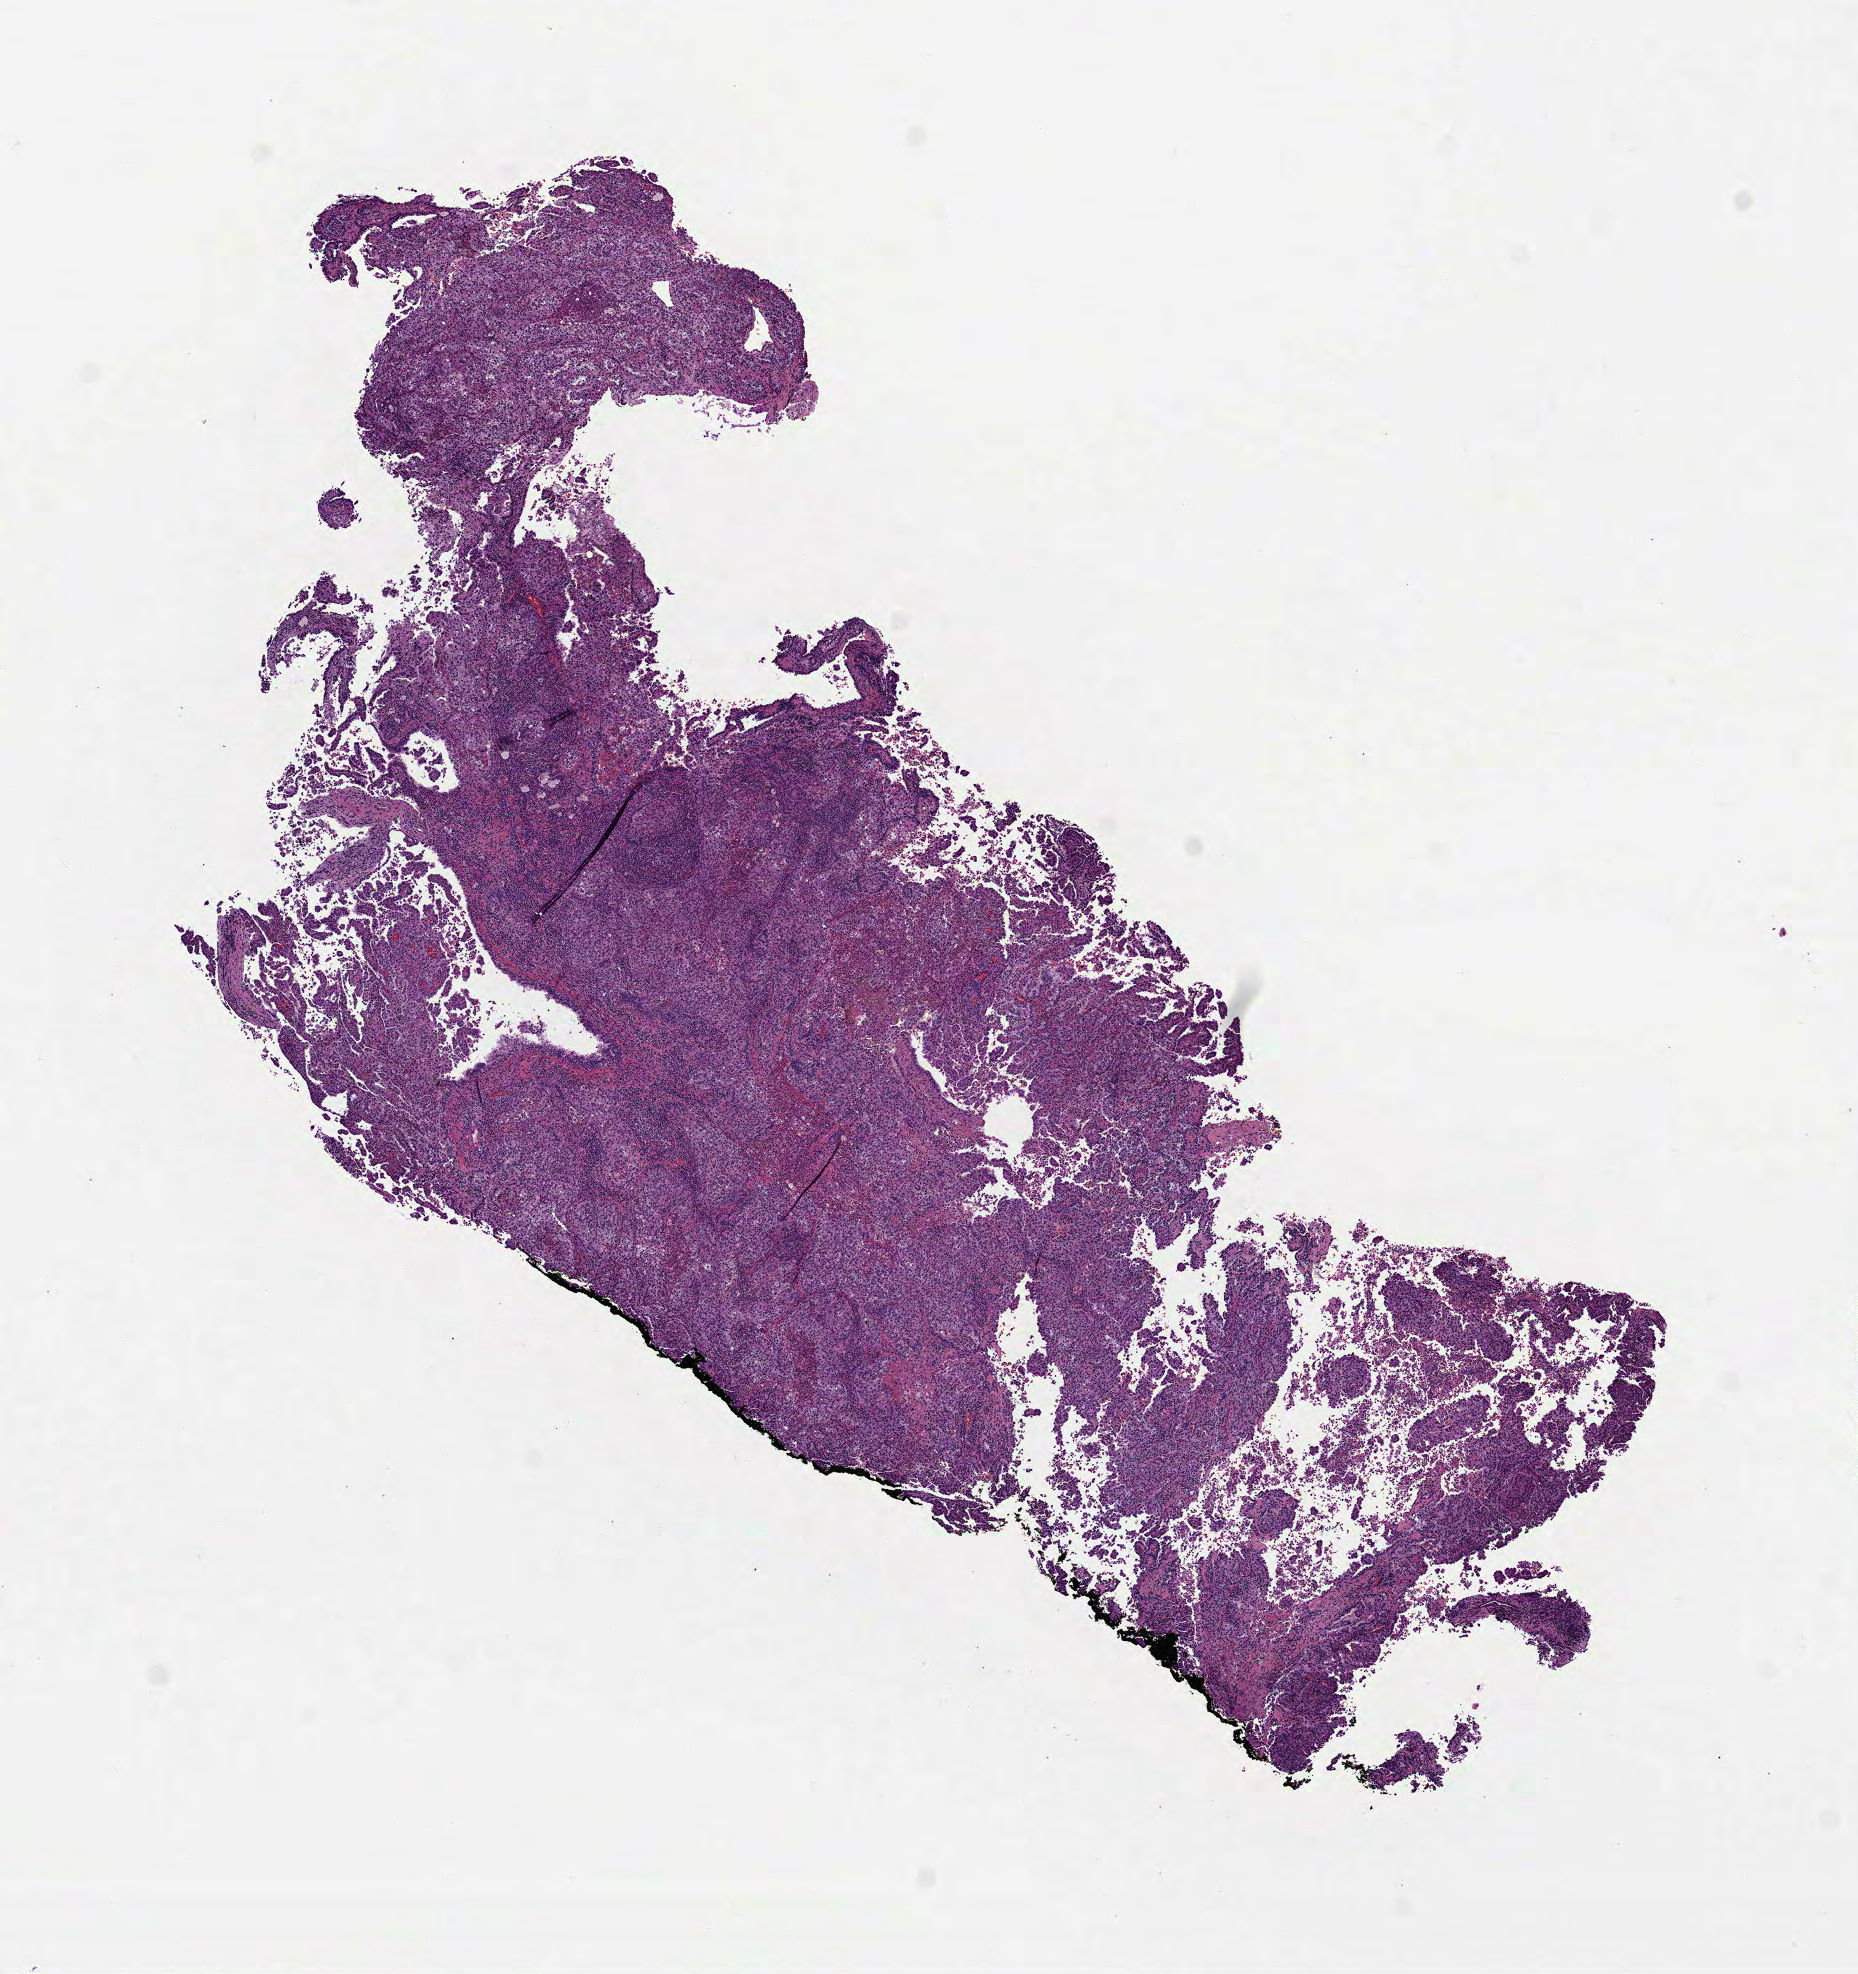
H&E whole-slide image, whole scanned area (about 7.5 x 8.0 mm, slide scanned at 40x) shown as a low-resolution overview. FFPE section. Kidney, primary tumour sample. Male, age 71 years at initial diagnosis.
• laterality: left
• TNM: T3a N1 MX
• AJCC pathologic stage: III (7th edition)
• lymph nodes positive (case pathology): 14 of 20 examined
• diagnosis: Papillary adenocarcinoma, NOS